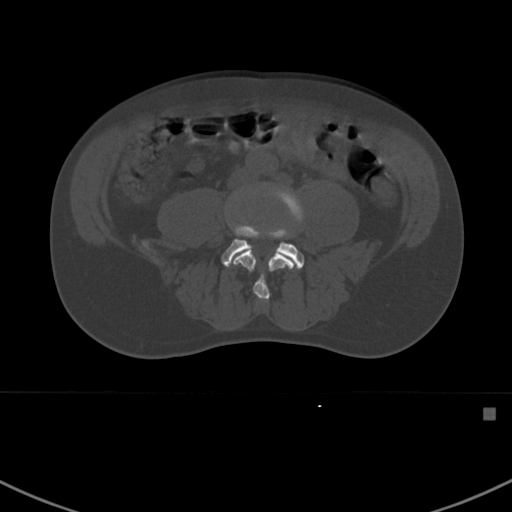
CT including the spine, one axial slice; position 231 of 412 along the scan axis; bone window (W 1800 / L 400 HU); 1.5 mm slice thickness; 512 × 512 image matrix. Patient: male, 59 years. From the clinical record (not read from this slice): primary cancer: prostate.
Outlined on this slice (semi-automatically segmented with operator editing):
- L4 vertebra: bounding box [x1, y1, x2, y2] px = [232, 186, 305, 302]
- L5 vertebra: [221, 225, 304, 269]